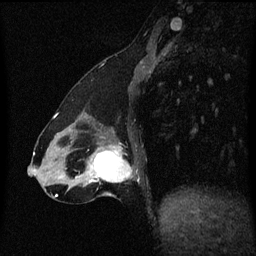
Breast MRI (dynamic contrast-enhanced), one sagittal slice; position 20 of 60 along the scan axis; dynamic contrast-enhanced series, image 2 of 3 at this slice position (ordered by acquisition); 1.5 T; TE 4.2 ms, TR 8.4 ms; 2 mm slice thickness; 256 × 256 image matrix. Female patient, age 47 years.
Annotated regions visible in this slice (semi-automatically segmented with operator editing):
- analysis volume of interest (the breast-tissue region the enhancement analysis was run in; not a lesion): bounding box (x1, y1, x2, y2) in pixels: (81, 140, 135, 197)
- tumour enhancement mask (voxels above the 70 % enhancement threshold inside the analysis volume of interest): (90, 146, 132, 183)